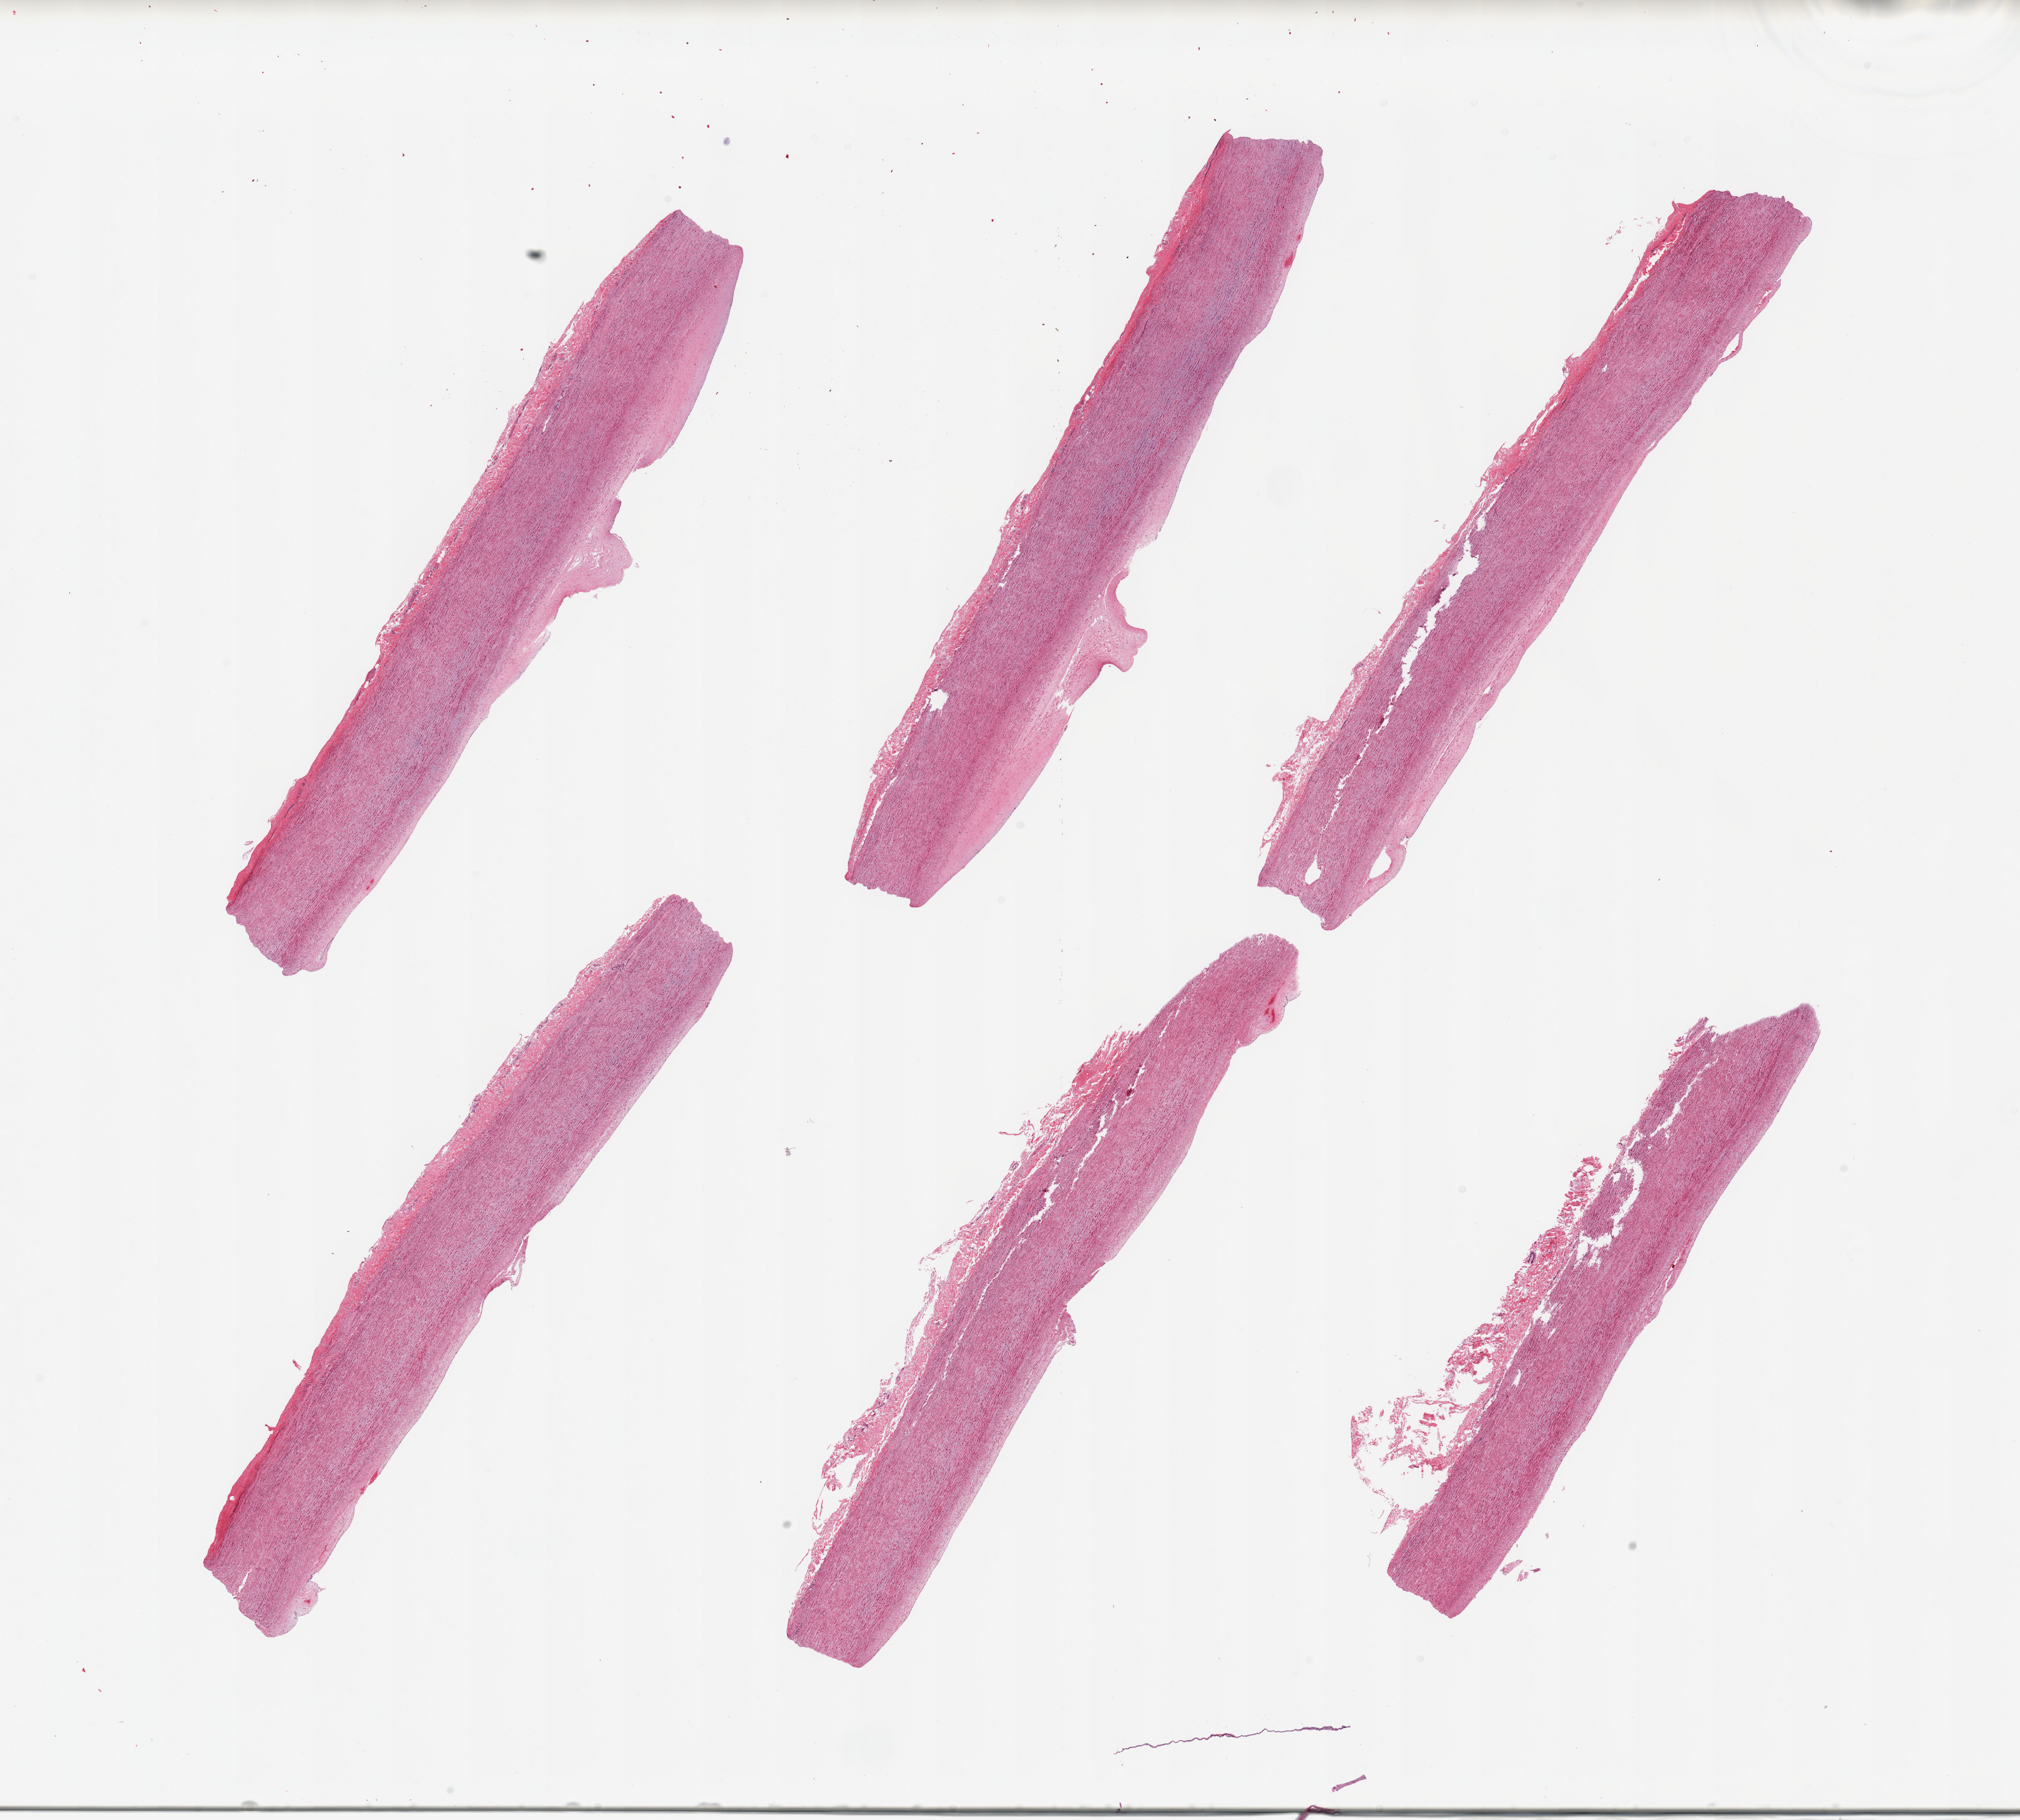
Digitized H&E-stained section, low-resolution overview of the scanned area, about 25.6 x 23.1 mm (from a 20x scan); PAXgene-fixed, paraffin-embedded tissue; target tissue: aorta; donor tissue sample. Donor sex: female.
Reviewer comment on this tissue sample: 6 pieces; mild focal plaque formation.